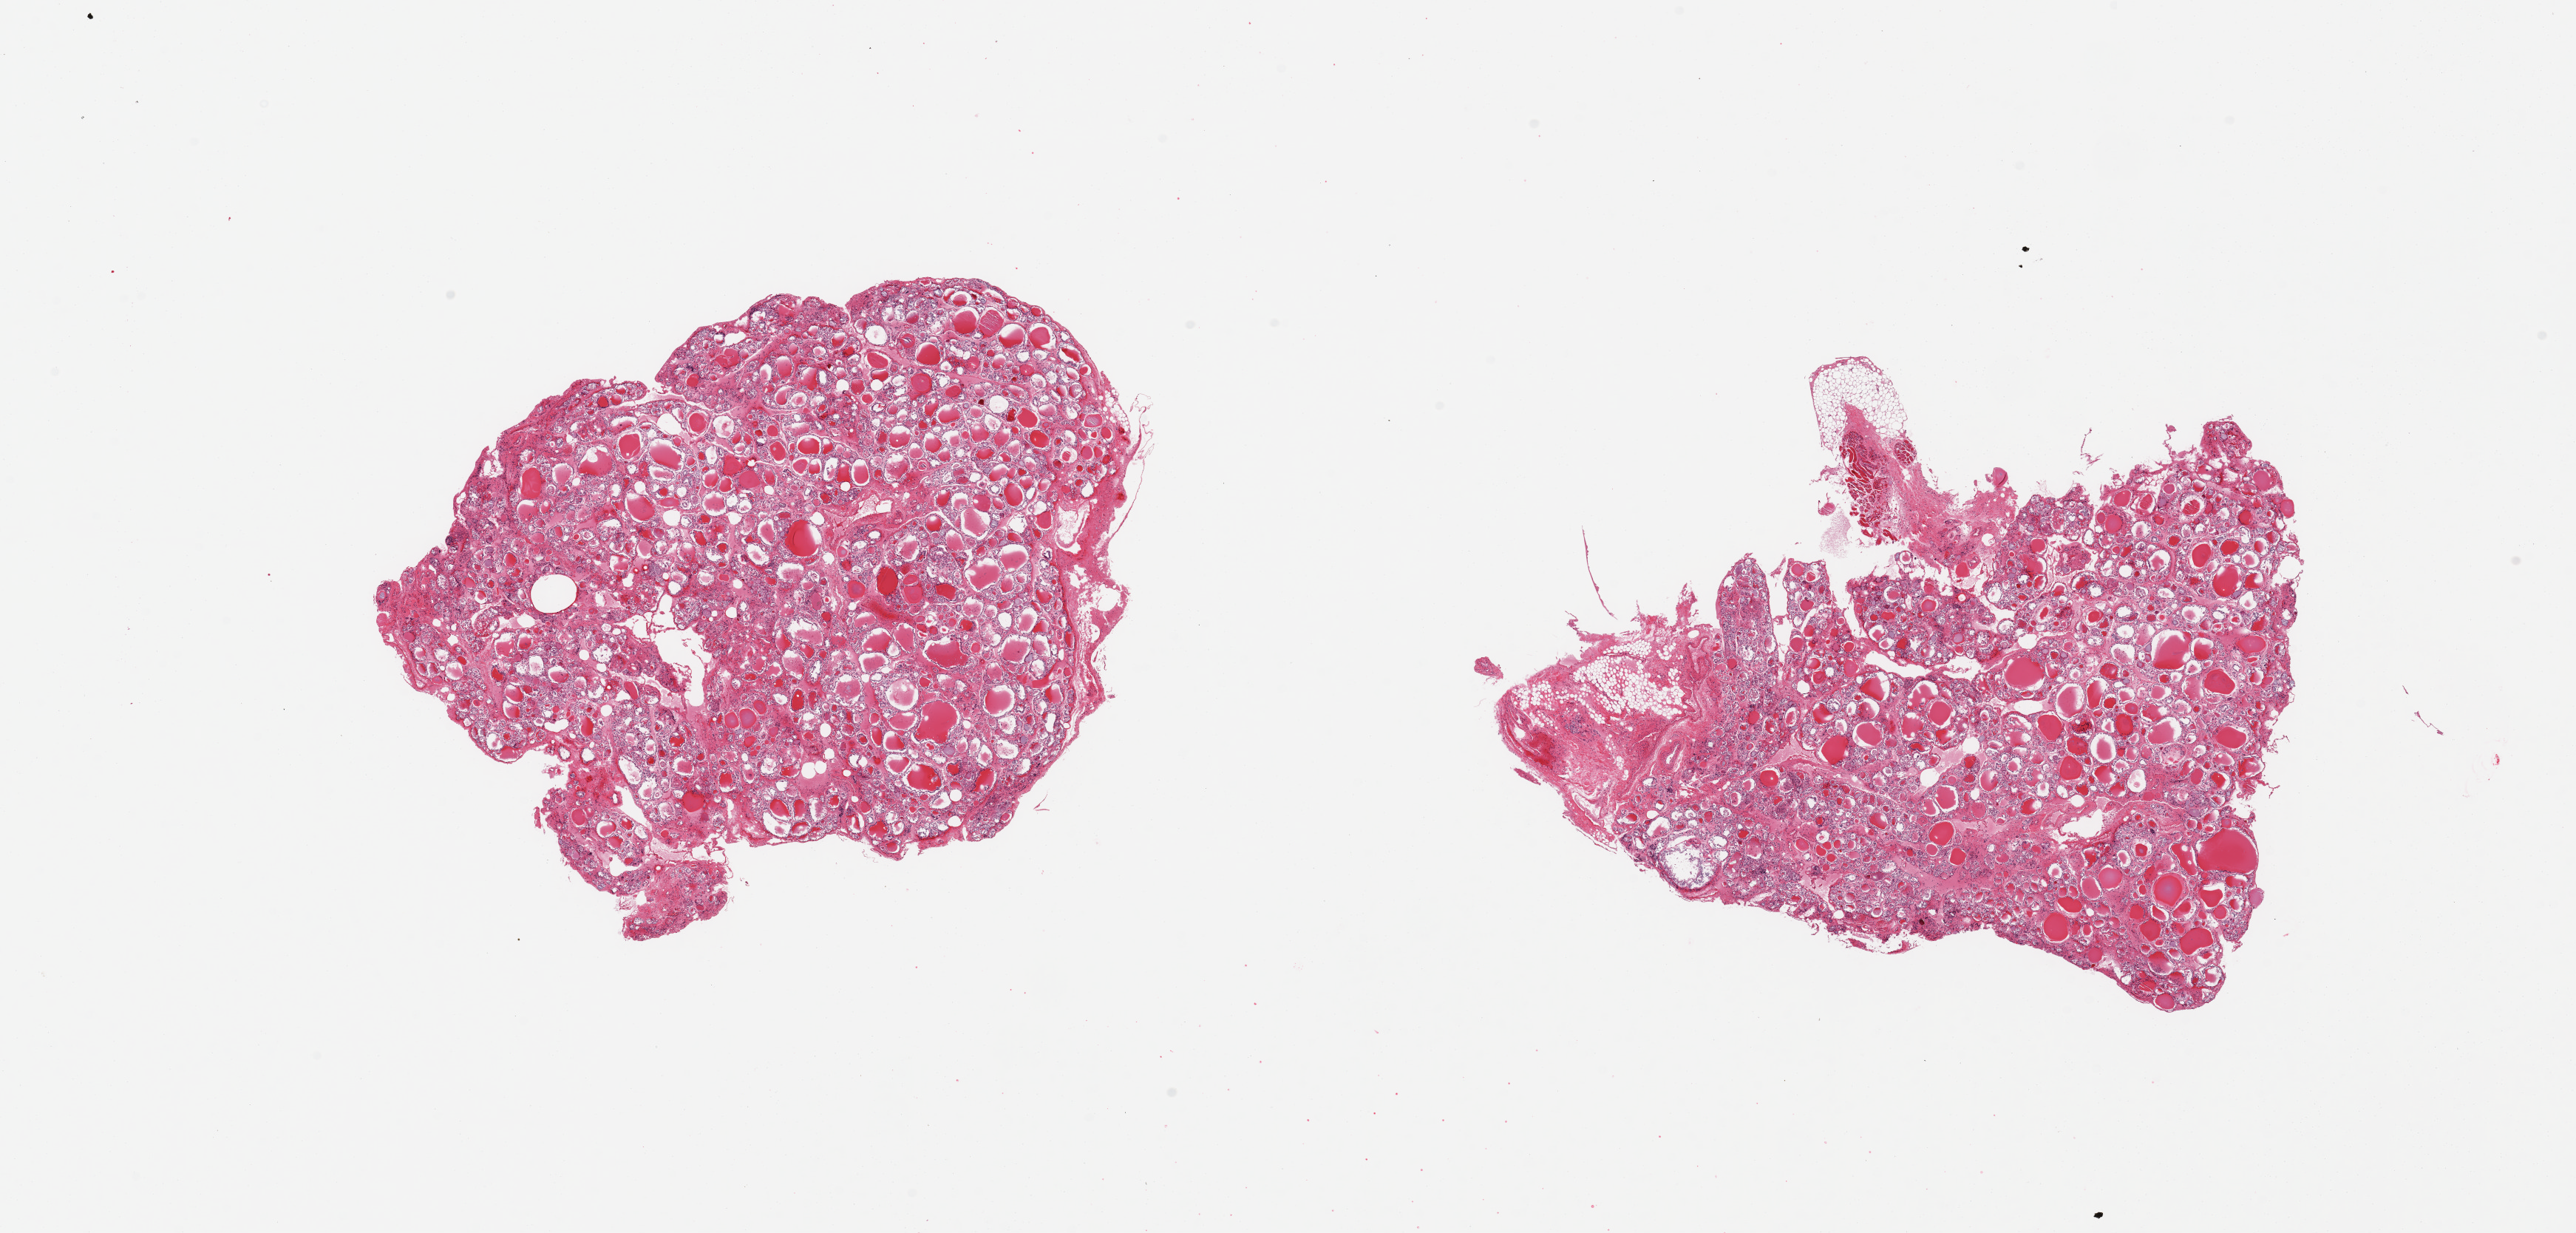
Whole-slide image, haematoxylin and eosin stain, brightfield, whole scanned area (about 27.6 x 13.2 mm) shown as a low-resolution overview, PAXgene-fixed paraffin-embedded (PFPE) section, section of thyroid (target tissue), tissue donor sample. Donor: male.
Reviewer comment on this tissue sample: 2 pieces; mild to moderate autolysis and sloughed follicular epithelium; small portion of attached fat and skeletal muscle fibers.